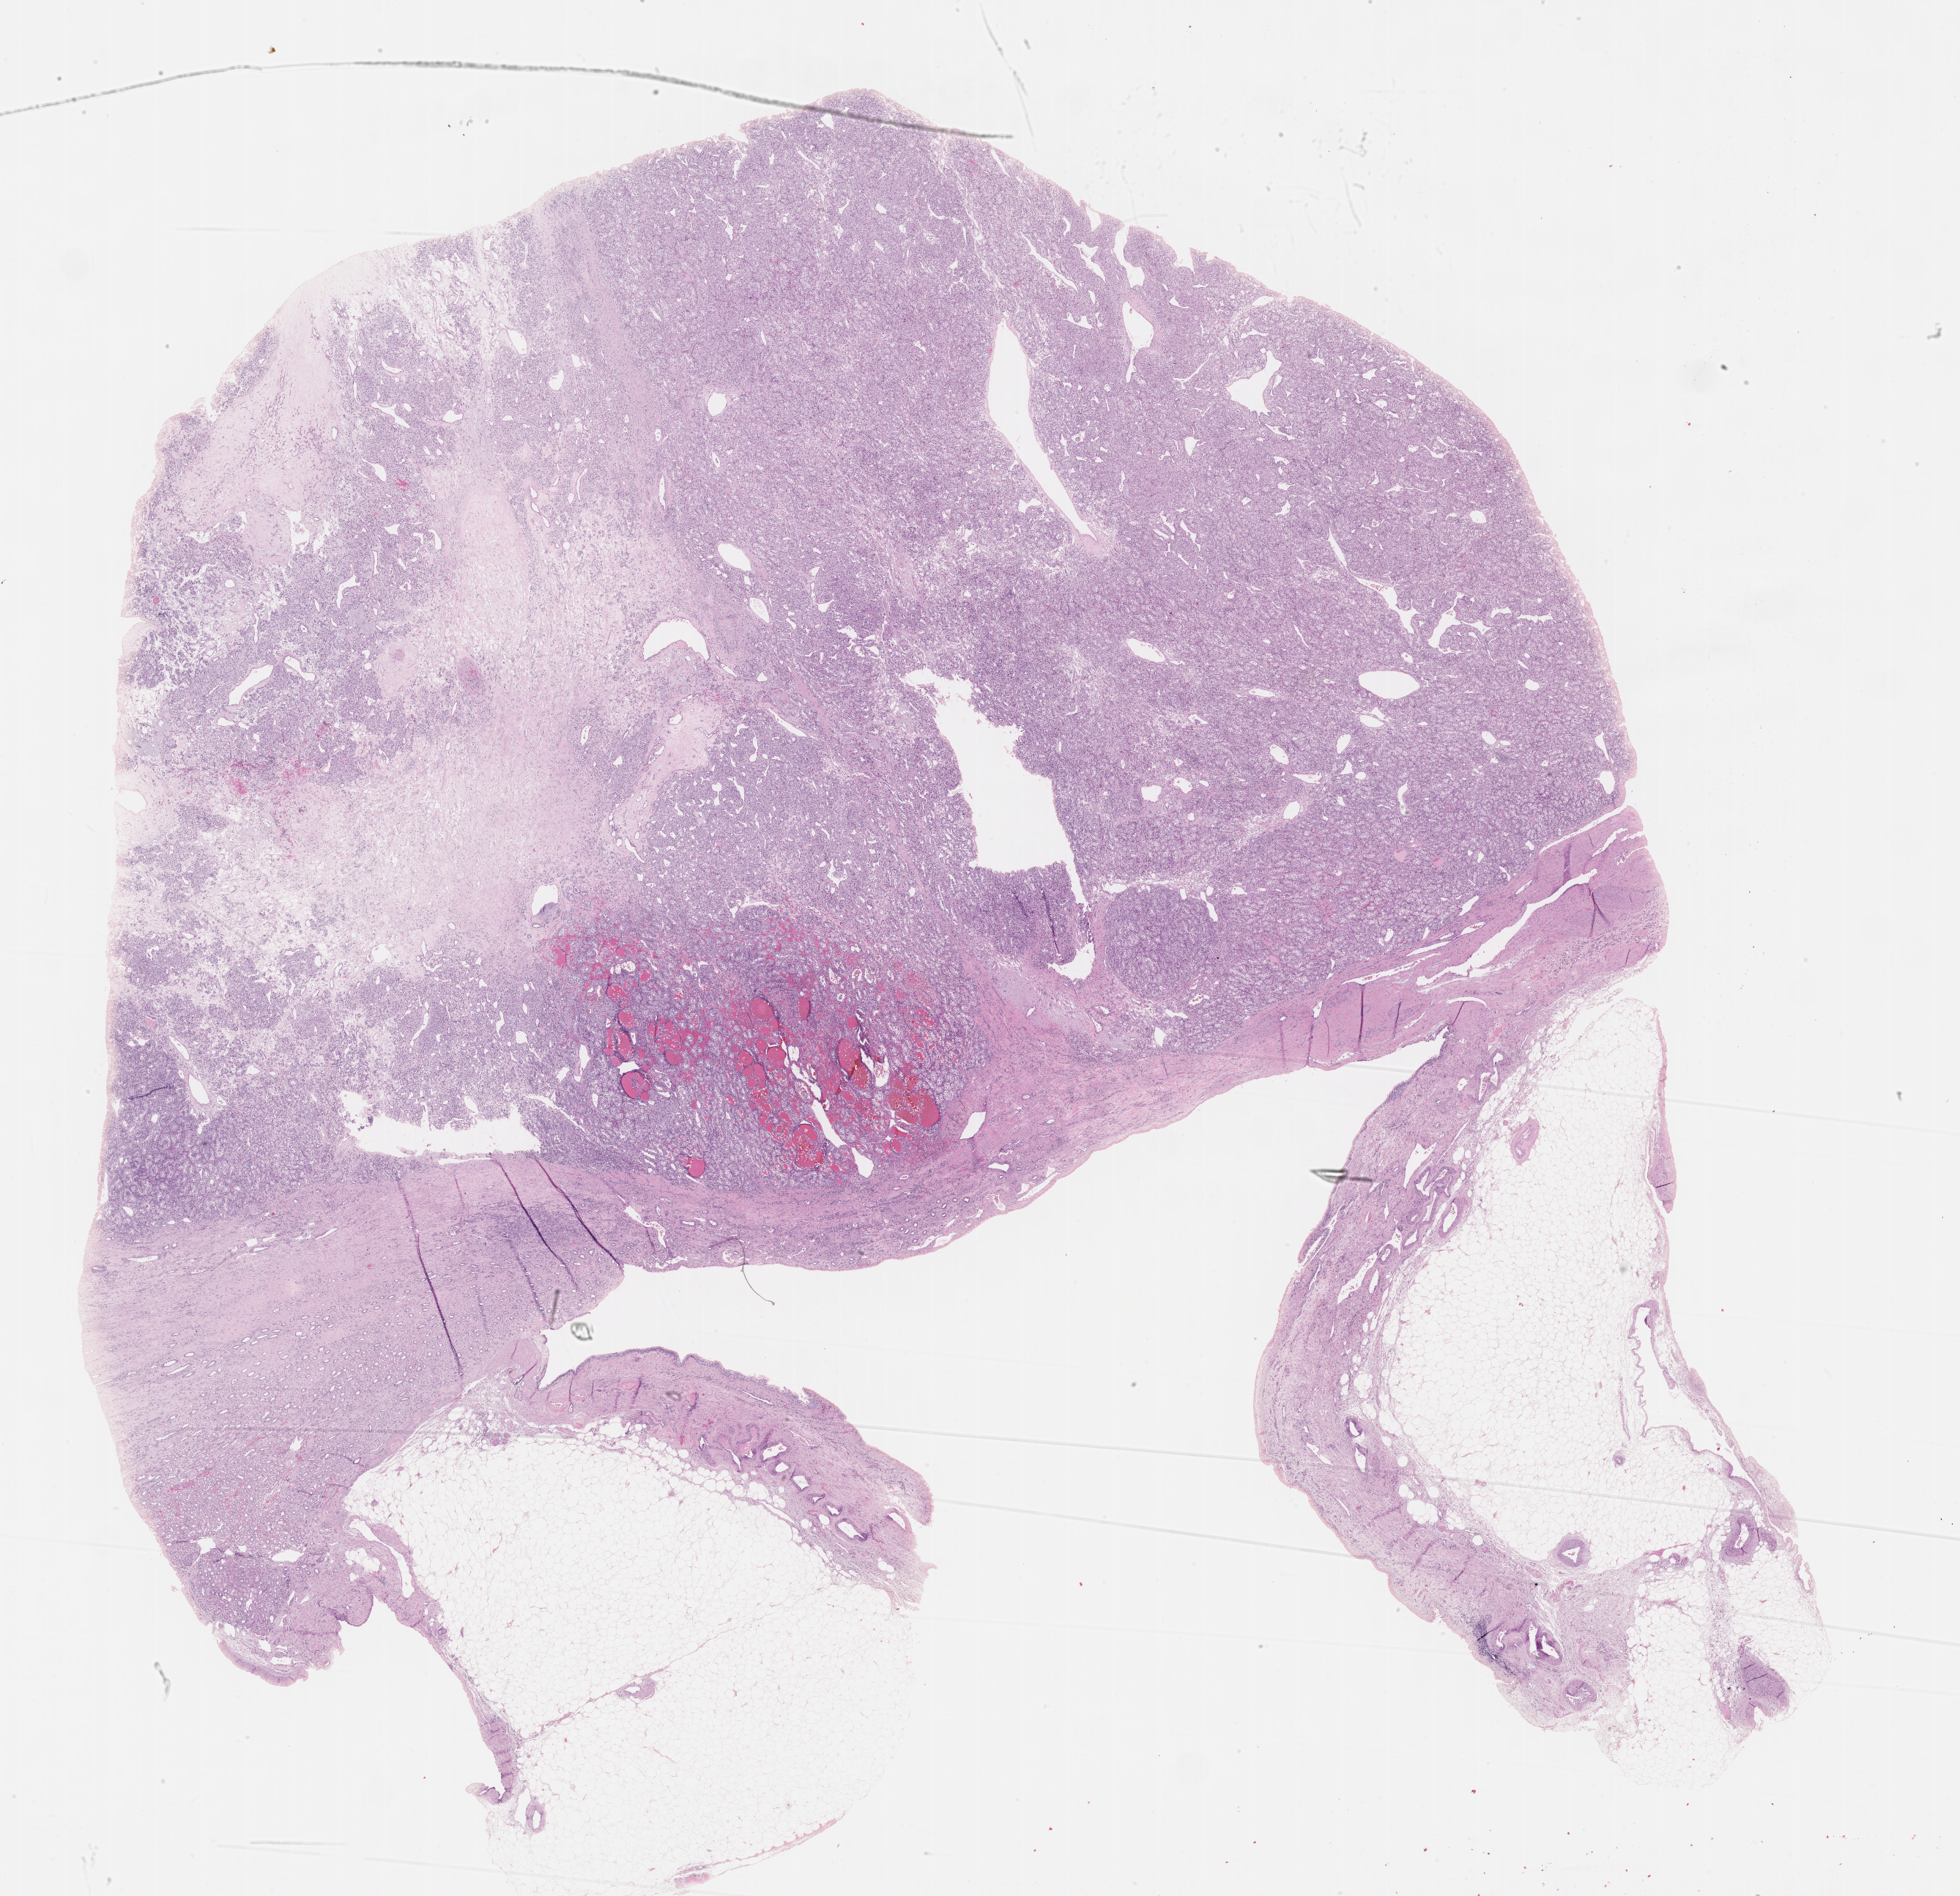
Hematoxylin and eosin (H&E) stained whole-slide image — a low-resolution overview of the entire scanned area, about 21.6 x 20.9 mm (acquisition: 40x scan), formalin-fixed paraffin-embedded (FFPE) diagnostic section, sample: primary tumour, kidney. Male, age 57 years at initial diagnosis. Histologic grade: G3 (poorly differentiated).
AJCC pathologic stage: II. Diagnosis: Clear cell adenocarcinoma, NOS.